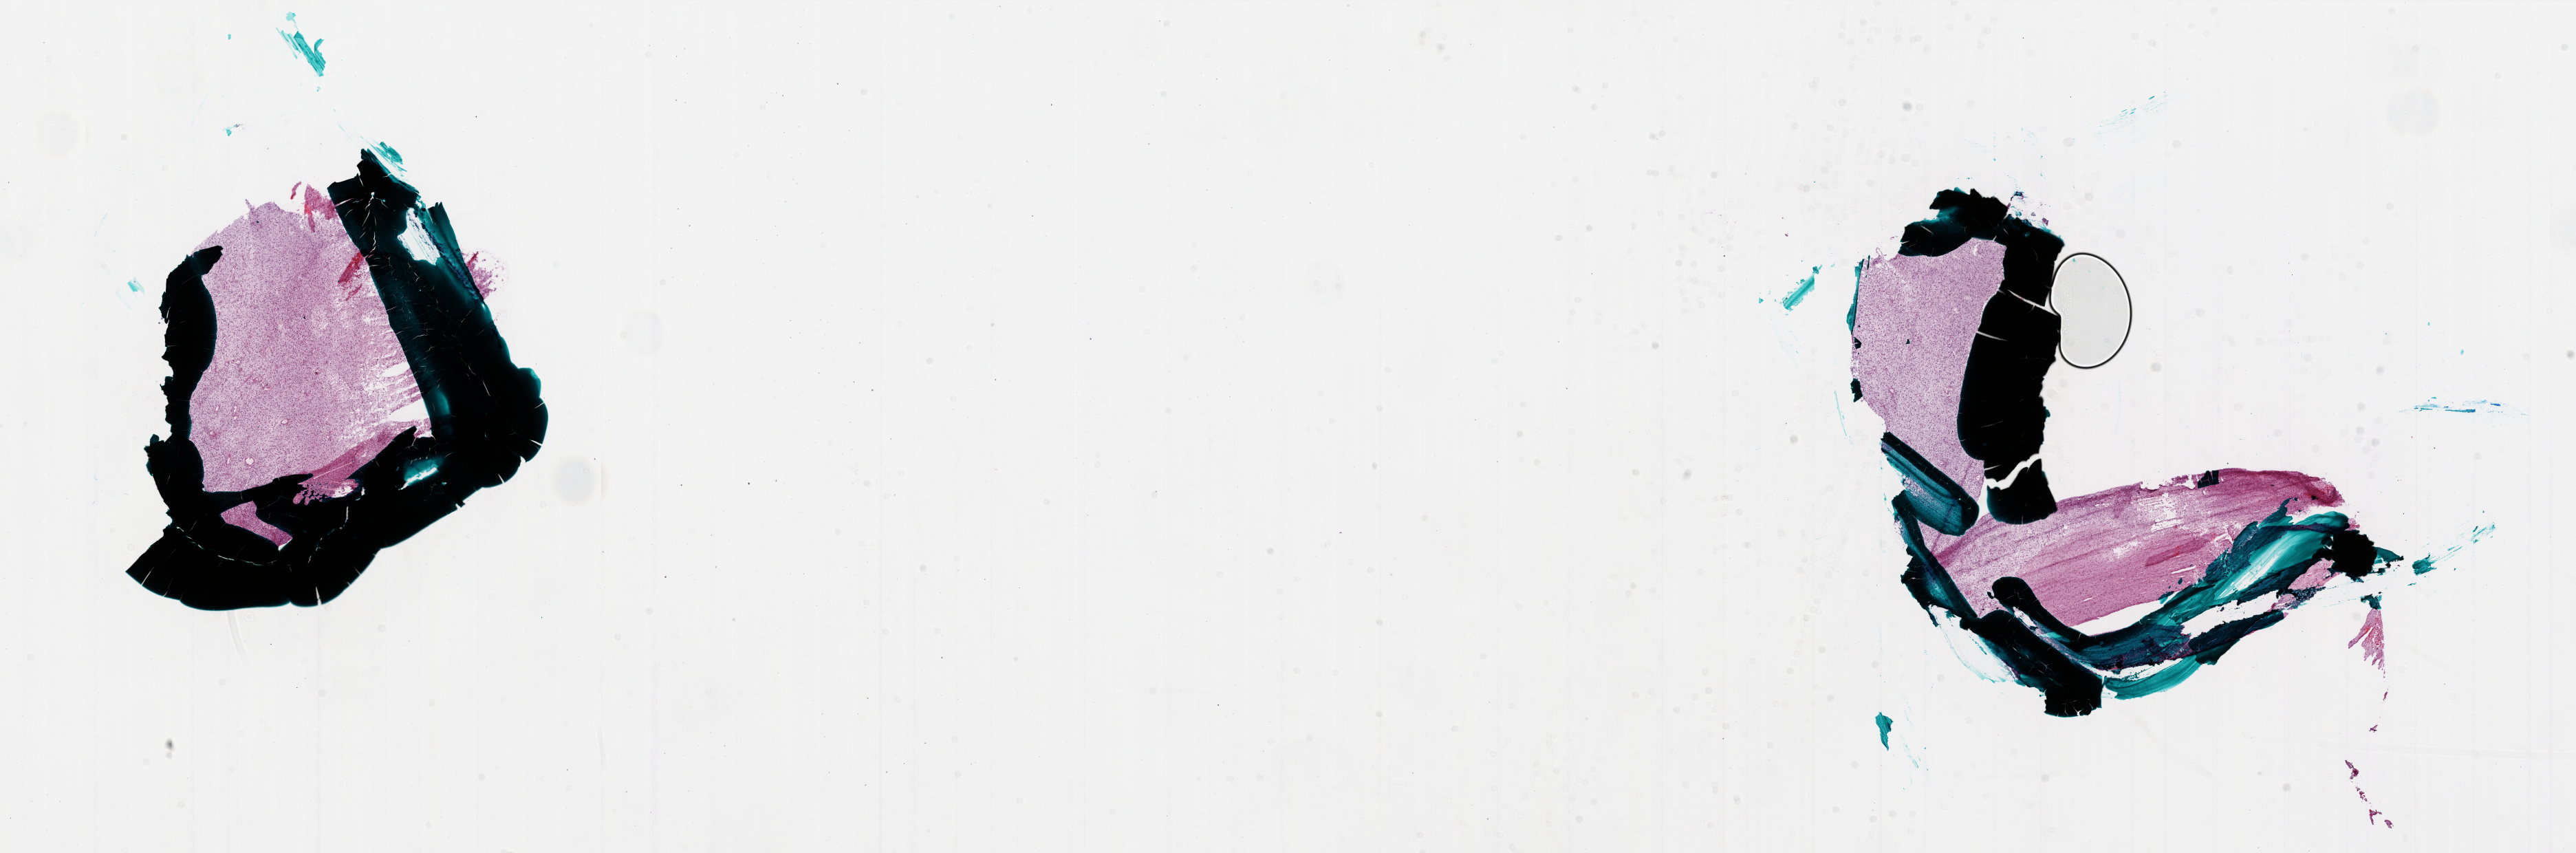
H&E-stained whole-slide image, a low-resolution overview of the entire scanned area, about 30.0 x 9.9 mm. Frozen section. Brain, primary tumour sample. Patient: male, age at initial diagnosis 73 years. Composition of this section per pathologist review: tumour cells 95%, tumour nuclei 100%, normal cells 0%, stromal cells 0%, necrosis 5%.
Pathologic diagnosis: Glioblastoma.